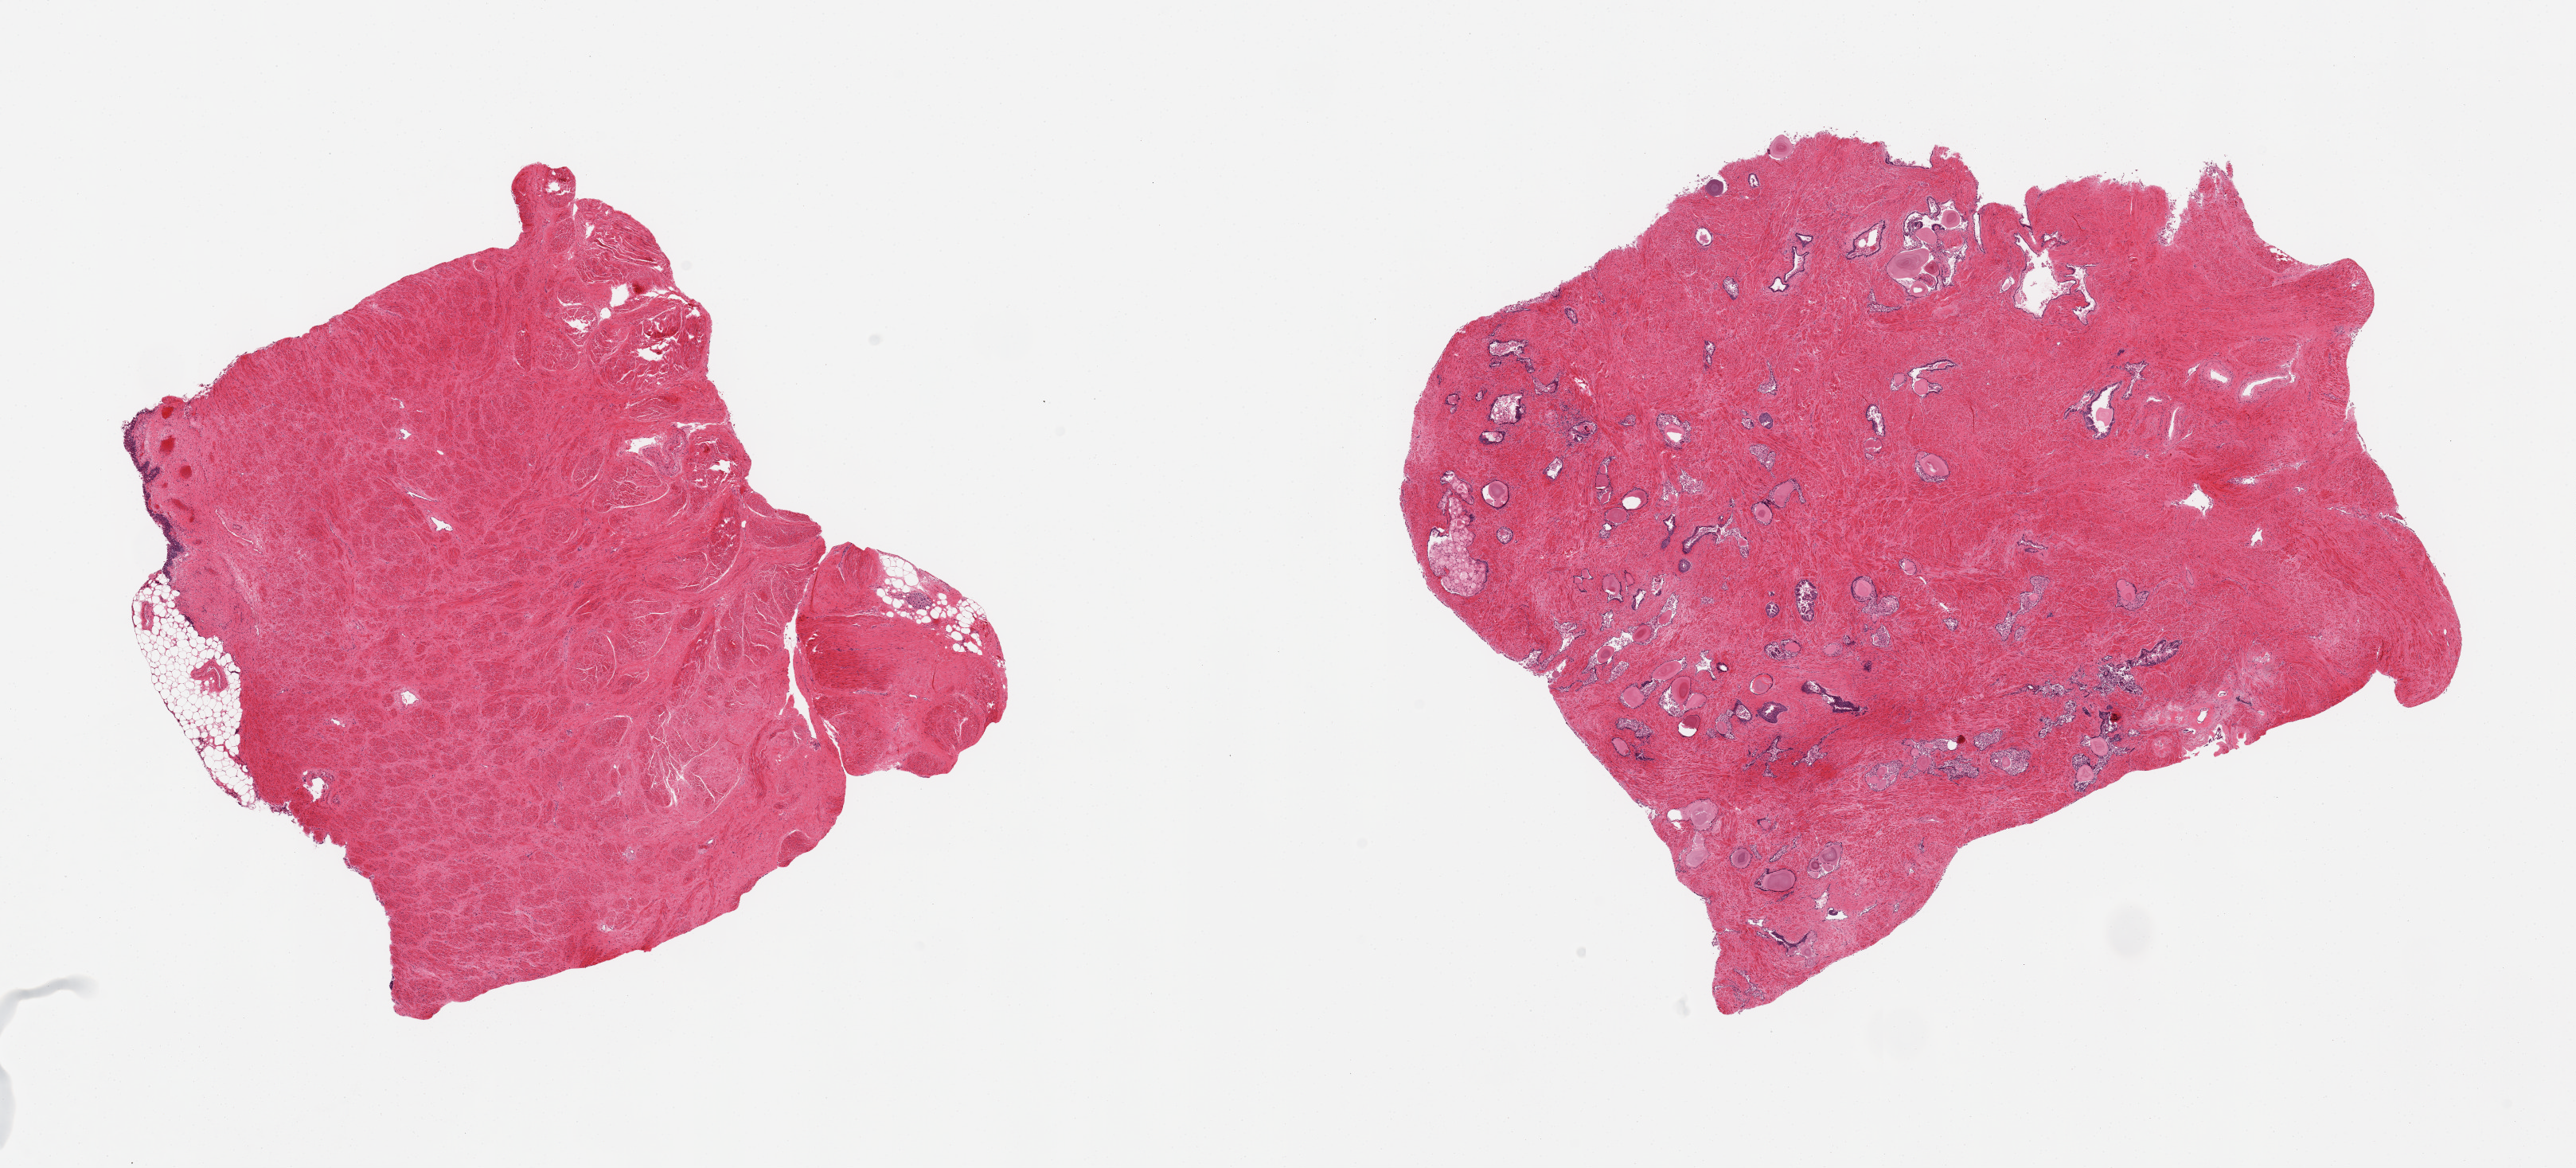
H&E whole-slide image, brightfield — shown as a low-resolution overview of the whole scanned area (about 25.6 x 11.6 mm, from a 20x scan). PAXgene-fixed paraffin-embedded (PFPE) section. Sampled site (target tissue): prostate. Donor tissue sample. Male donor.
Reviewer comment on this tissue sample: 2 pieces, glandular elements with moderately advanced autolysis; glands present in one section; other is all stroma.